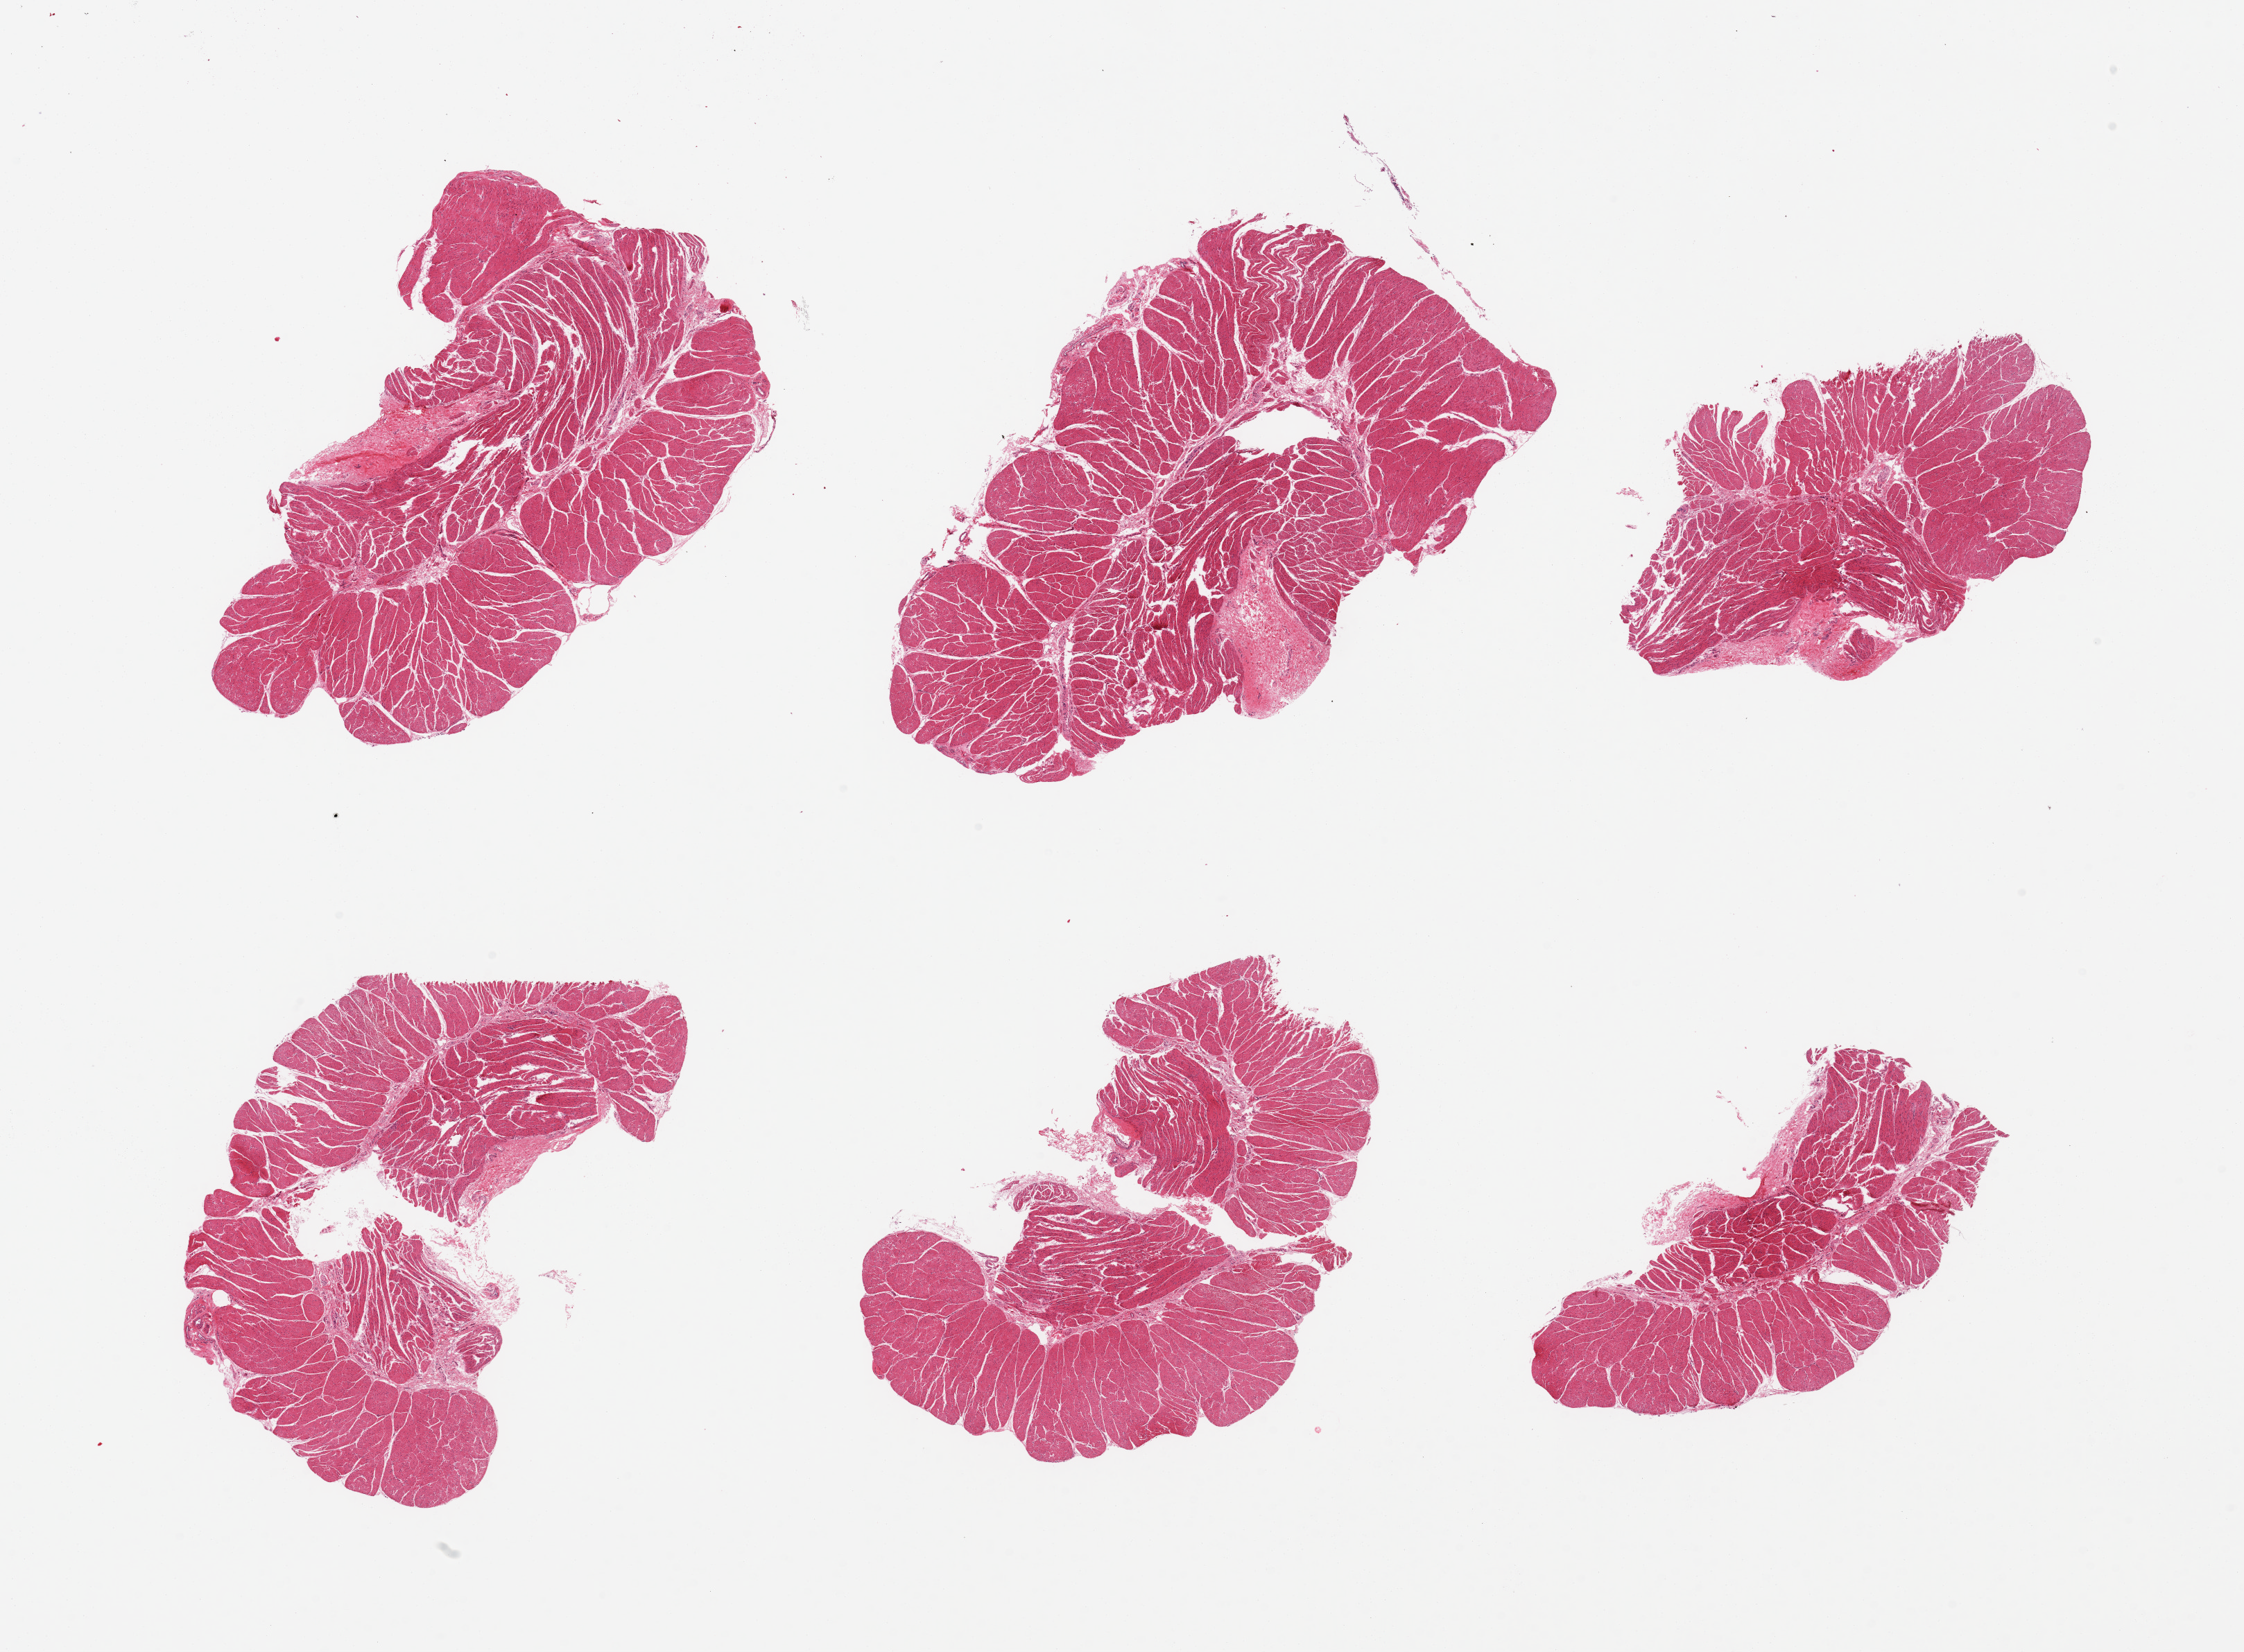
Hematoxylin and eosin (H&E) whole-slide image — low-resolution overview of the scanned area, about 25.6 x 18.8 mm; PAXgene-fixed, paraffin-embedded tissue; target tissue: esophageal muscle; donor tissue sample. Male donor.
Review note (as recorded): 6 pieces; well dissected with small foci of submucosal stroma.